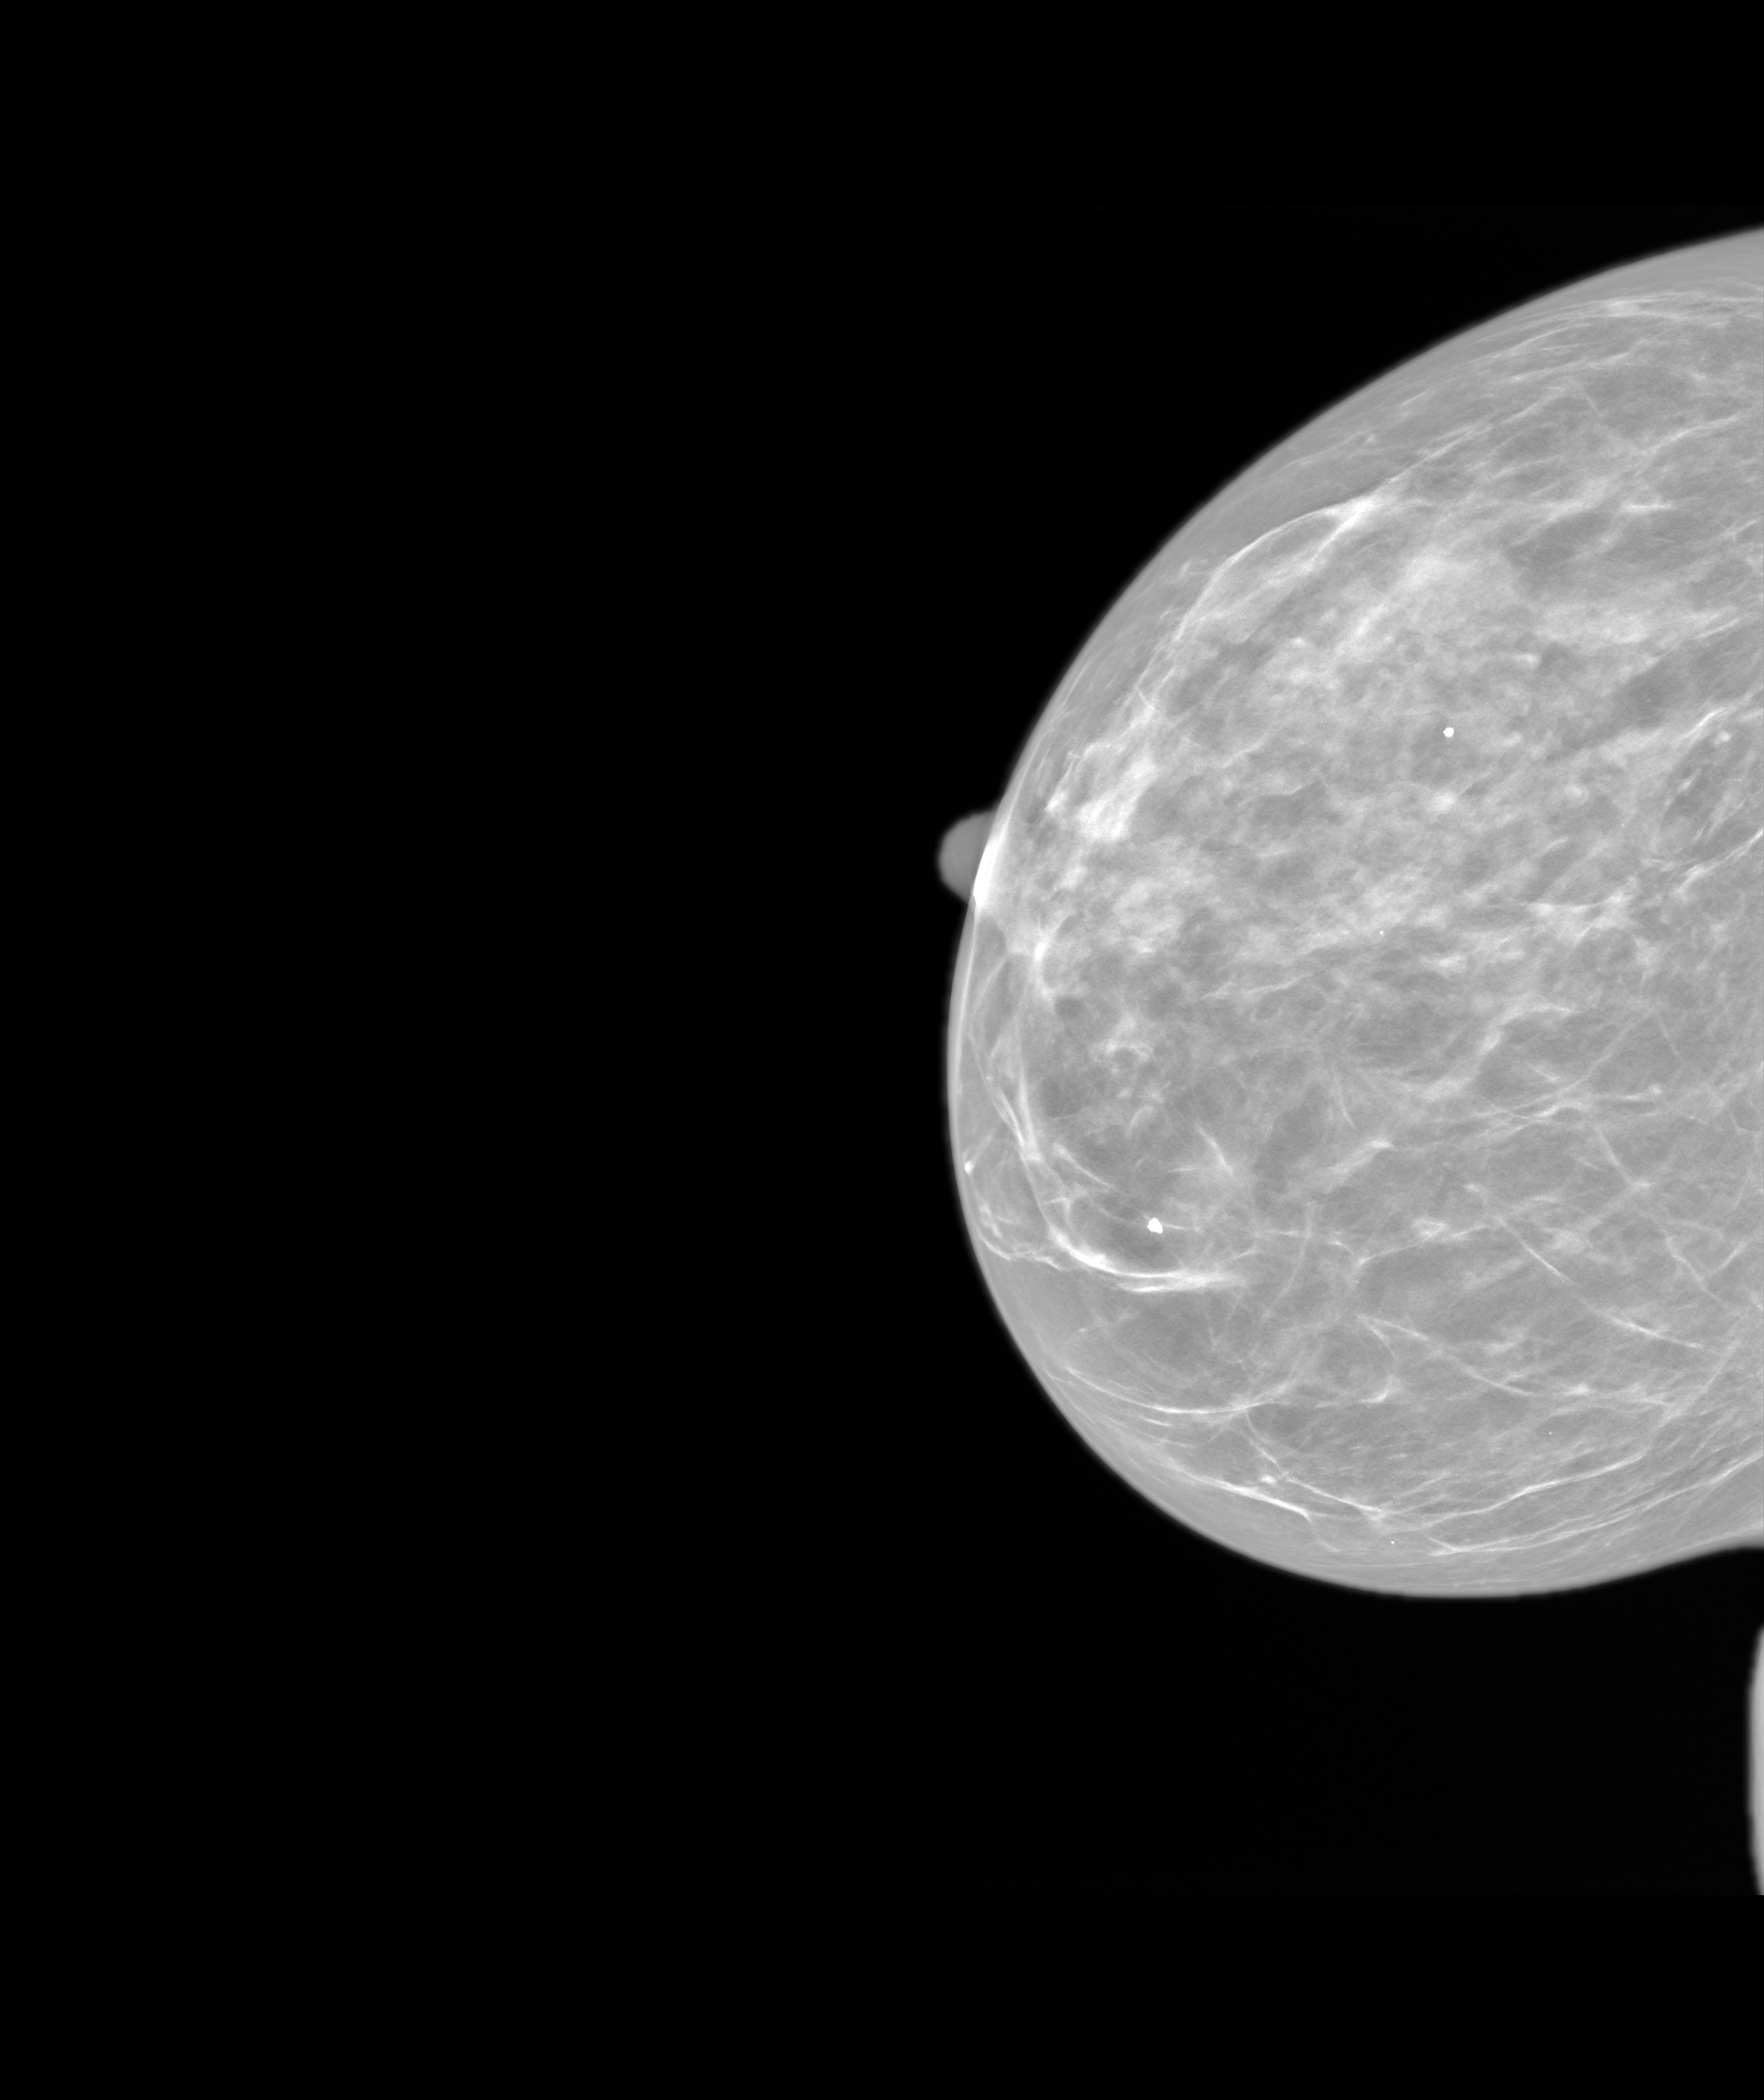
Screening examination, system: SenoIris_1SP1.1(421).
Image type: synthesized 2-D view from tomosynthesis. Breast: right. Projection: CC view.